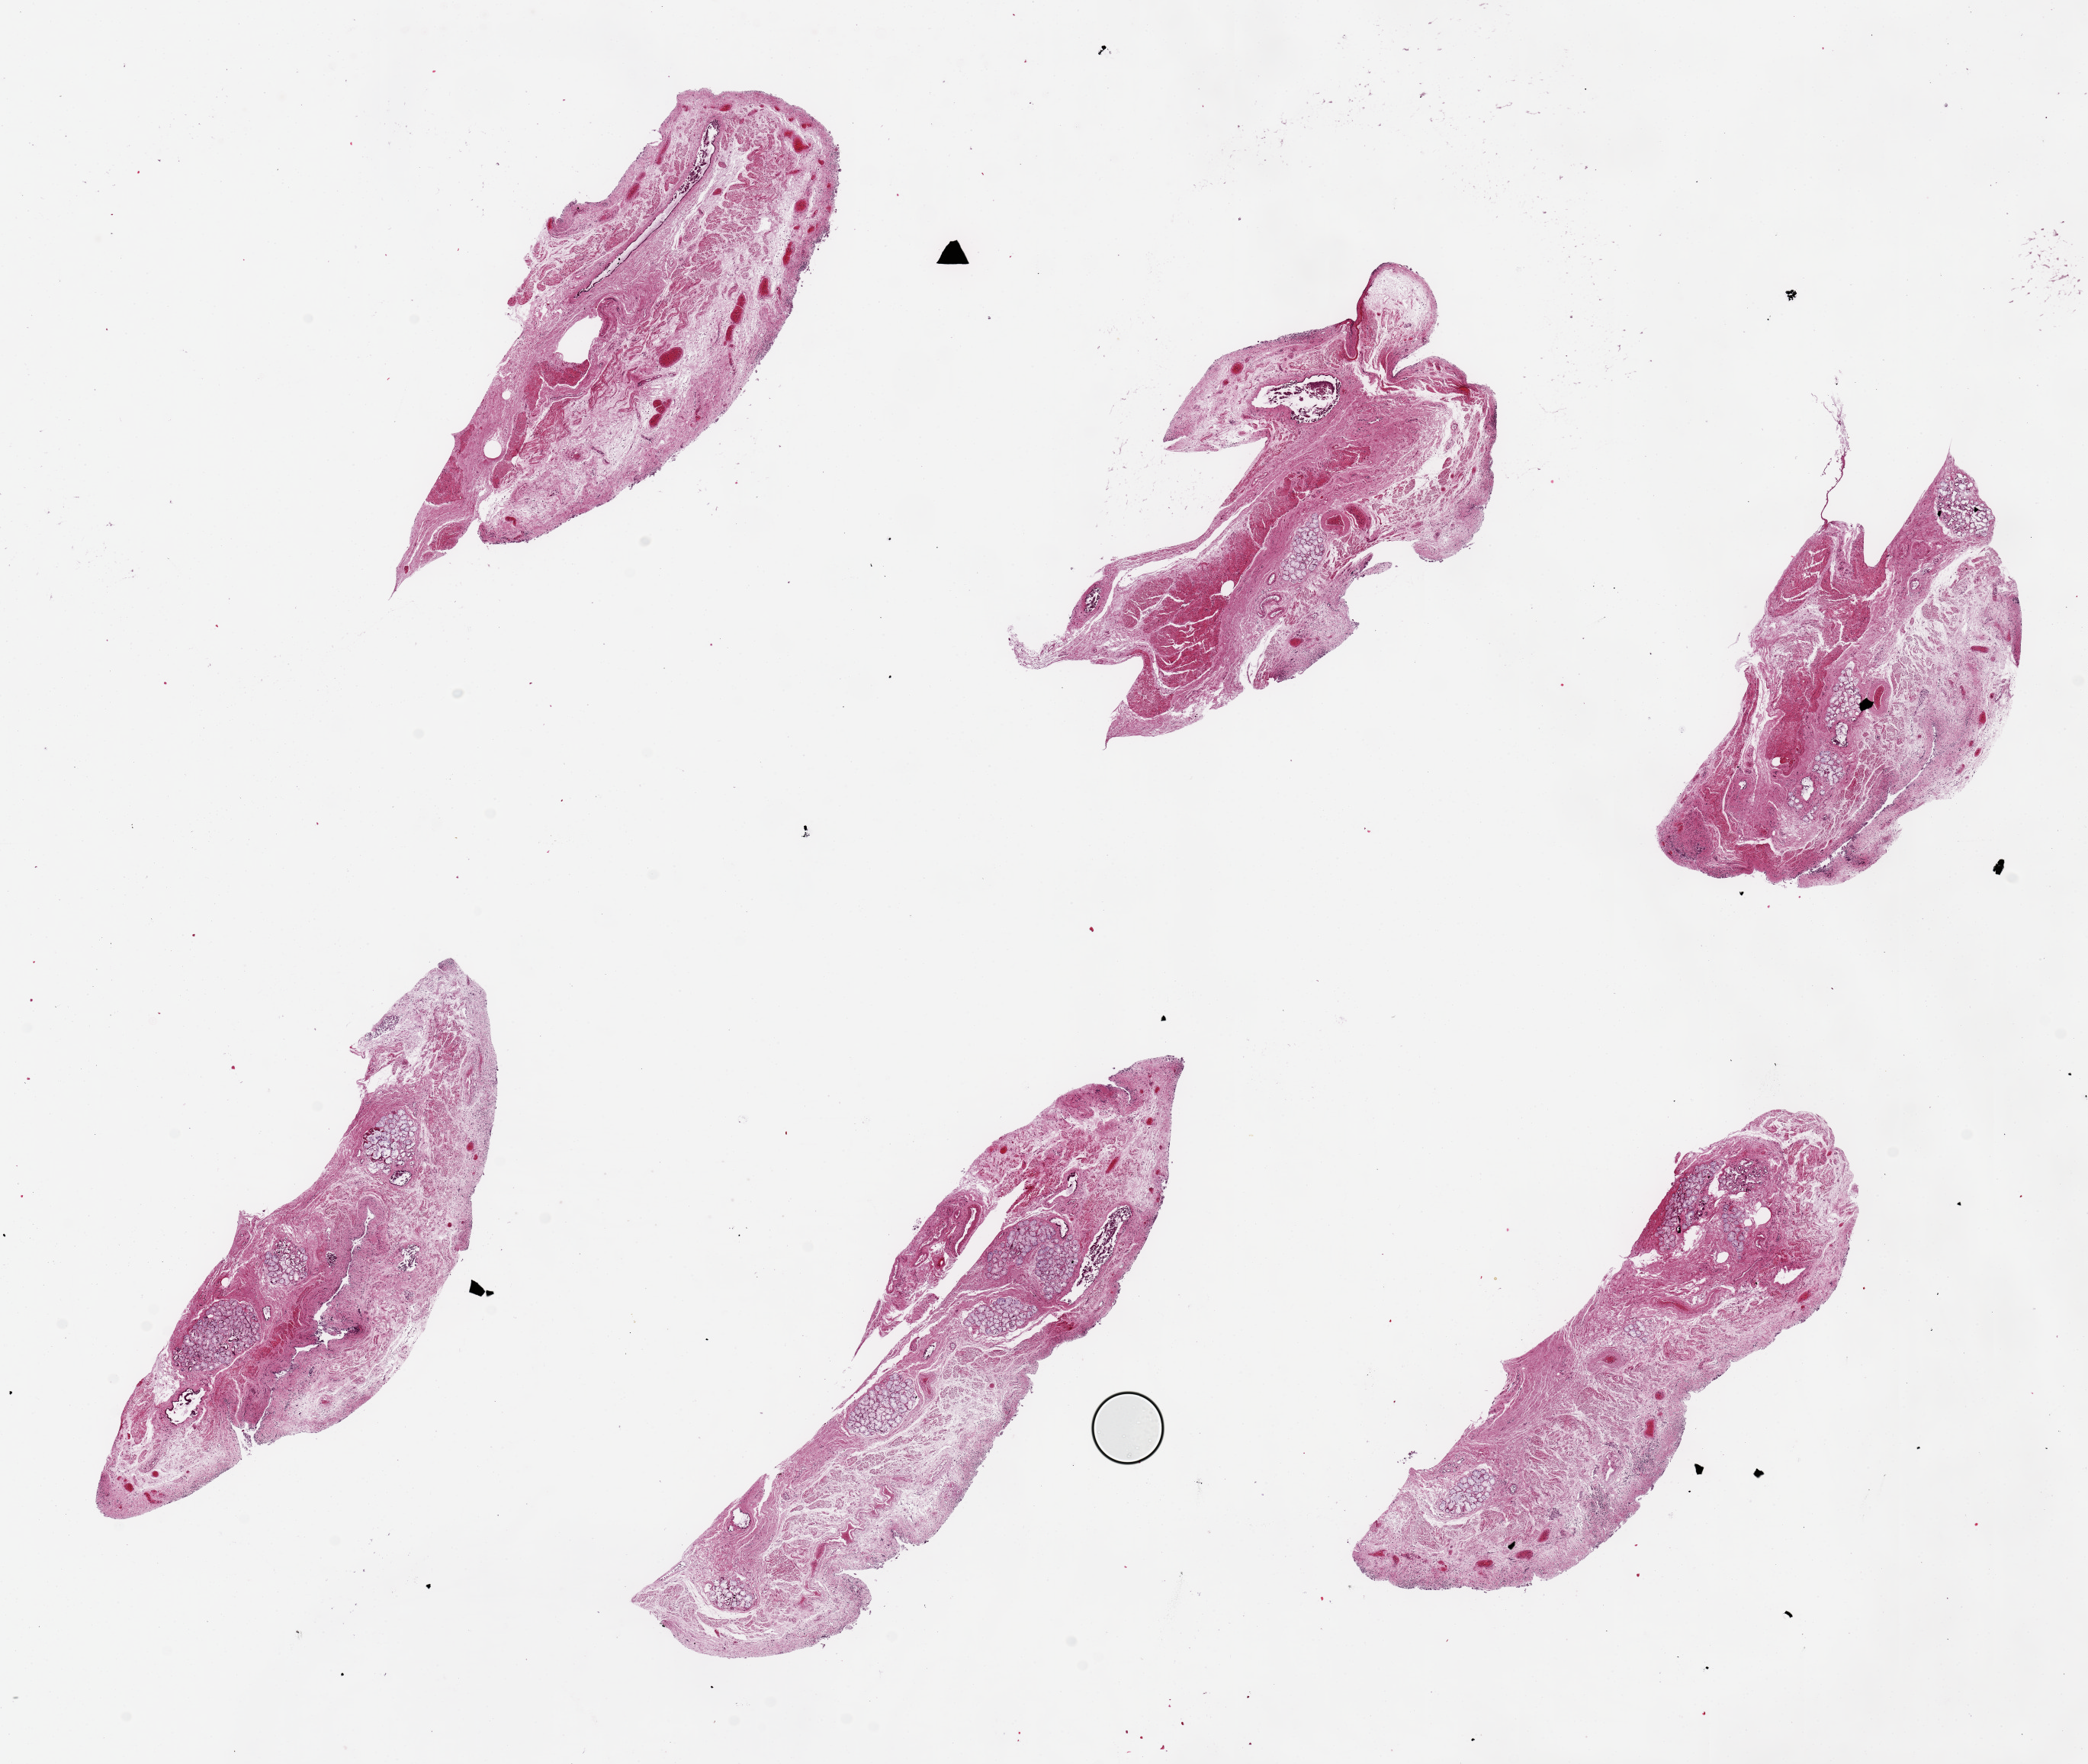
Digitized H&E-stained section, low-resolution overview of the scanned area, about 21.7 x 18.3 mm (slide scanned at 20x), PAXgene-fixed paraffin-embedded (PFPE) section, target tissue: esophageal mucous membrane, tissue donor sample. Male donor.
Review note (as recorded): 6 pieces, up to 8x2mm; too autolyzed for further study; epithelium totally sloughed.